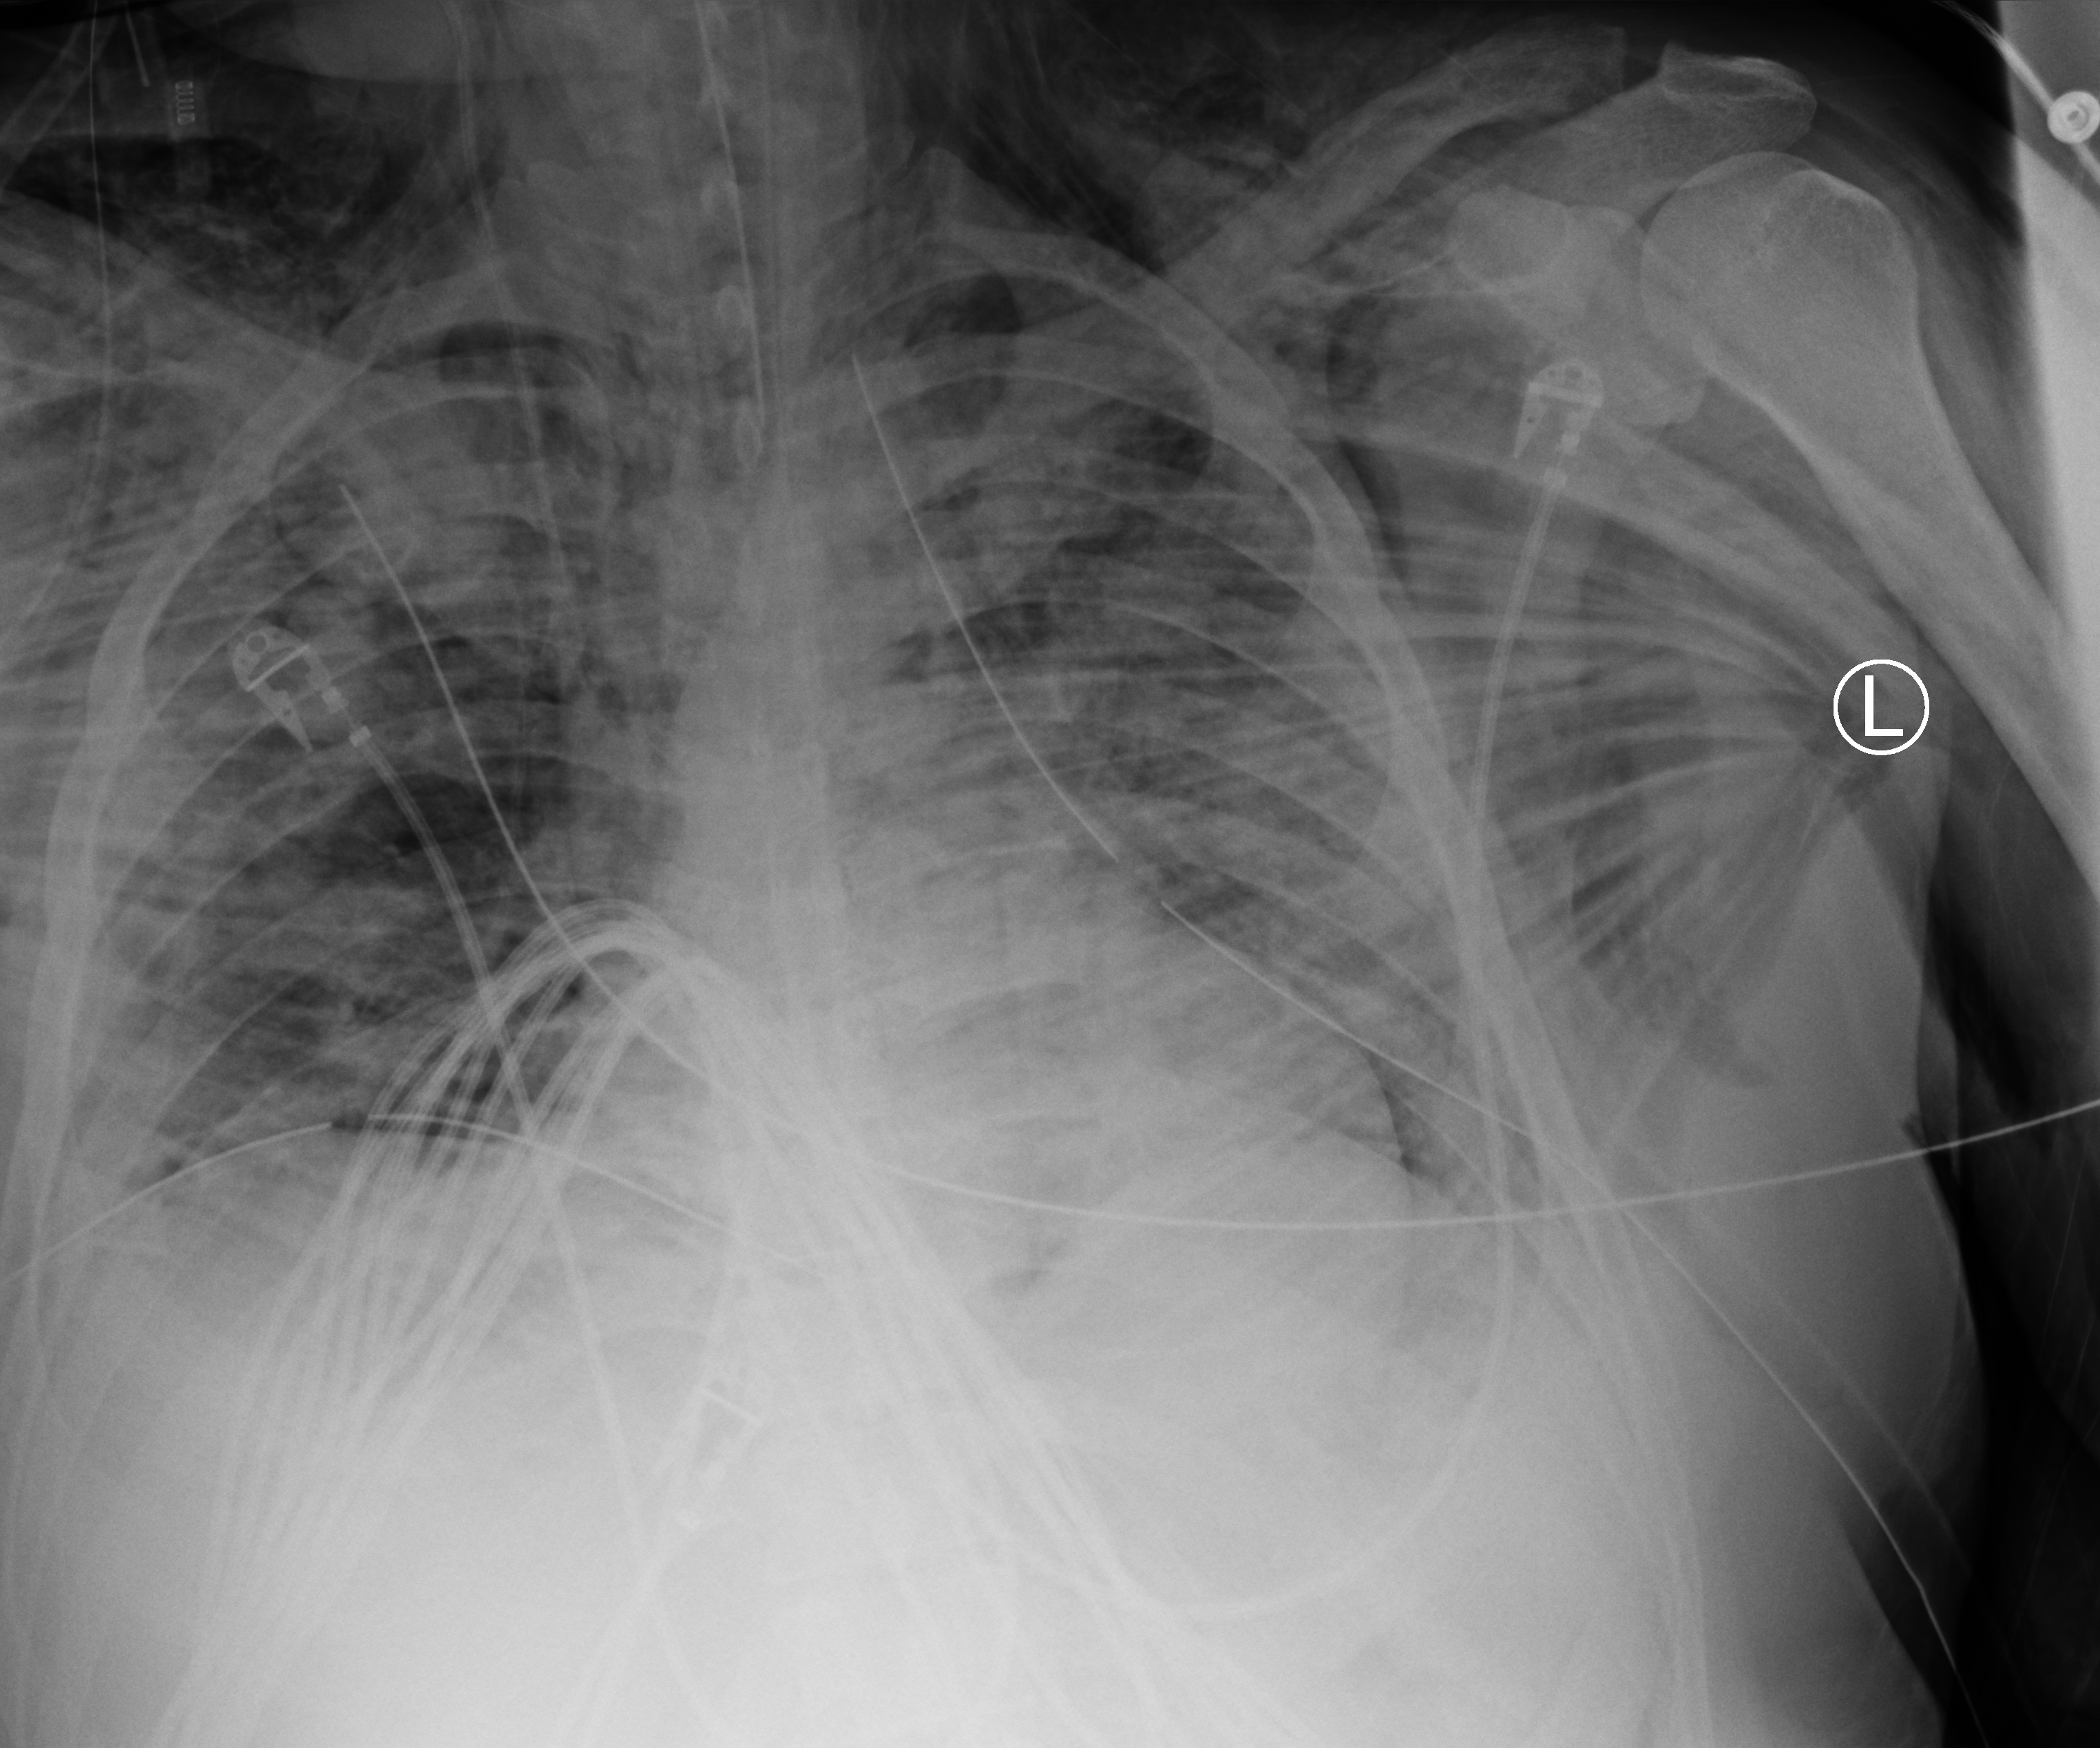
Bedside chest radiograph (computed radiography), anteroposterior (AP) projection. Patient hospitalised with COVID-19; male, aged 18–59 years.
From the hospital-stay record, not from the radiograph (when in the stay this image was taken is not recorded):
- admitted to intensive care during this hospital stay: yes
- mechanically ventilated during this hospital stay: yes
- length of hospital stay: 29 days